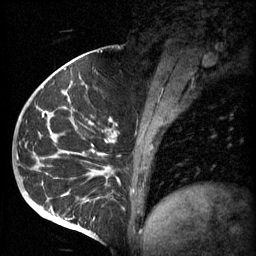
Breast MRI (dynamic contrast-enhanced), one sagittal slice. Position 26 of 60 along the scan axis. 3 images stored at this slice position (order not interpretable as contrast timing). 1.5 T. TE 4.2 ms, TR 11 ms. 2 mm slice thickness. 256 × 256 image matrix, field of view 200 × 200 mm. Female patient, age 51 years.
Annotated regions visible in this slice (semi-automatically segmented with operator editing):
- analysis volume of interest (the breast-tissue region the enhancement analysis was run in; not a lesion): bounding box [x1, y1, x2, y2] px = [48, 82, 161, 197]
- tumour enhancement mask (voxels above the 70 % enhancement threshold inside the analysis volume of interest): [48, 100, 154, 175]